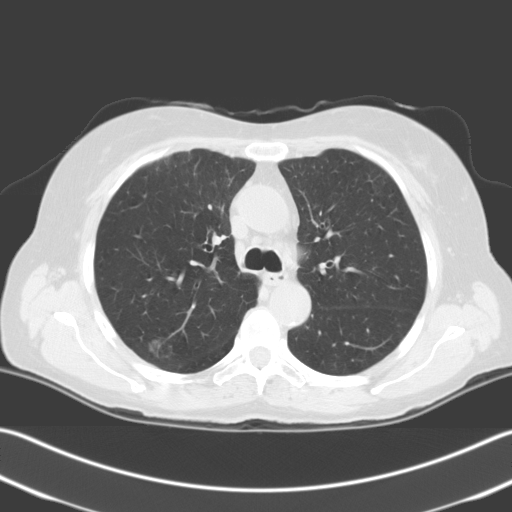
Axial slice from a low-dose chest CT screening exam. Baseline screening round. Lung window (W 1500 / L -600 HU). Standard (soft-tissue) reconstruction kernel (C). Slice 57 of 204 in the series. Female participant, aged 67 years at enrolment. Current smoker at enrolment.
Lesion marked by an expert reader, bounding box <123,326,180,374> (left, top, right, bottom; pixels). The screening reader recorded 2 non-calcified nodules or masses ≥4 mm on this exam (right upper lobe, right upper lobe); which of them this box marks is not recorded. Official screen result: positive, change unspecified: nodule(s) >= 4 mm or enlarging nodule(s), mass(es), or other non-specific abnormalities suspicious for lung cancer. Participant outcome: lung cancer diagnosed 24 days after this screen — squamous cell carcinoma, NOS, right upper lobe, stage IIIA (AJCC 6th edition), 56 mm at pathology.